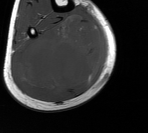
MRI of an extremity soft-tissue mass, one axial slice; slice 64 of 76 in the series (ordered by position); MR volume resampled by the dataset authors to the PET/CT grid (not the native acquisition matrix); 148 × 133 image matrix, field of view 145 × 130 mm. Male patient. From the clinical record (not read from this slice): histological type: liposarcoma - round cell; grade: high; site of the primary tumour: right calf.
Annotated regions visible in this slice (expert contour drawn on MRI and transferred to this co-registered scan by the dataset authors):
- gross tumour volume (mass): bounding box (x1, y1, x2, y2) in pixels: (15, 17, 103, 93)